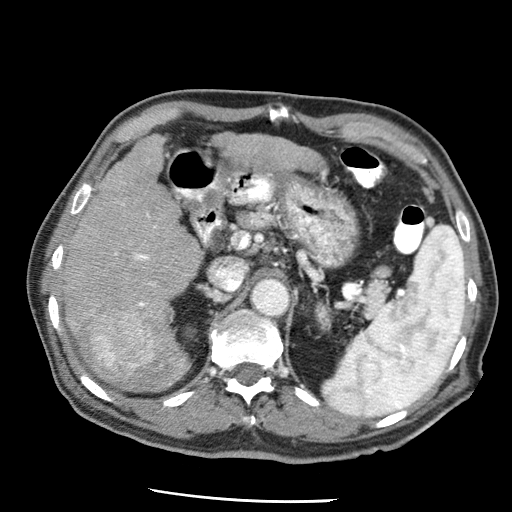
Contrast-enhanced abdominal CT (liver protocol), one axial slice. Slice 29 of 79 in the series (ordered by position). Reconstruction kernel STANDARD. 120 kVp. Soft-tissue window (W 400 / L 40 HU). 512 × 512 image matrix. From the clinical record (not read from this slice): diagnosis: hepatocellular carcinoma (patient treated with transarterial chemoembolisation; whether this scan precedes or follows treatment is not stated here); TNM stage (as recorded): Stage-IIIA; Child-Pugh class: A; tumour differentiation: moderately differentiated.
Structures marked on this image (semi-automatic segmentation, software-assisted and operator-edited):
- liver parenchyma outside the tumour (the mass and vessels are separate outlines, so this box may not span the whole liver): bounding box <58,135,202,386> (left, top, right, bottom; pixels)
- mass: <89,309,154,371>
- liver vessels: <114,204,155,307>